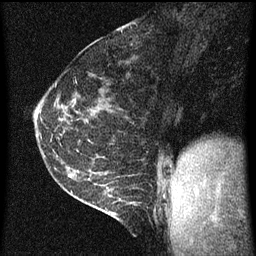
Breast MRI (dynamic contrast-enhanced), one sagittal slice; position 24 of 60 along the scan axis; dynamic contrast-enhanced series, image 2 of 3 at this slice position (ordered by acquisition); 1.5 T; TE 4.2 ms, TR 8 ms; 2 mm slice thickness; 256 × 256 image matrix, field of view 180 × 180 mm. Female patient, age 35 years.
Structures marked on this image (semi-automatically segmented with operator editing):
- analysis volume of interest (the breast-tissue region the enhancement analysis was run in; not a lesion): box from (x=106, y=182) to (x=141, y=223) px
- tumour enhancement mask (voxels above the 70 % enhancement threshold inside the analysis volume of interest): (x=108, y=196)–(x=137, y=215)